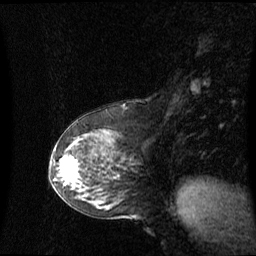
Breast MRI (dynamic contrast-enhanced), one sagittal slice. Slice 32 of 60 in the series (ordered by position). Dynamic contrast-enhanced series, image 2 of 3 at this slice position (ordered by acquisition). 1.5 T. TE 4.2 ms, TR 8.4 ms. 2.1 mm slice thickness. 256 × 256 image matrix, field of view 260 × 260 mm. Female patient, age 59 years. Case-level facts recorded for this patient, not image findings: setting: breast cancer imaged before/during neoadjuvant chemotherapy; receptor status: HR-positive, HER2-negative.
Outlined on this slice (semi-automatic segmentation, software-assisted and operator-edited):
- analysis volume of interest (the breast-tissue region the enhancement analysis was run in; not a lesion): bounding box <55,148,87,191> (left, top, right, bottom; pixels)
- tumour enhancement mask (voxels above the 70 % enhancement threshold inside the analysis volume of interest): <62,161,79,179>